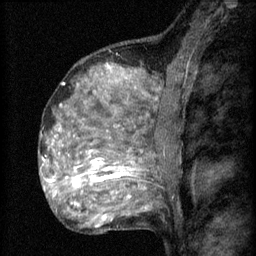
Breast MRI (dynamic contrast-enhanced), one sagittal slice; position 40 of 60 along the scan axis; 3 images stored at this slice position (order not interpretable as contrast timing); 1.5 T; TE 4.2 ms, TR 8.2 ms; 2 mm slice thickness; 256 × 256 image matrix, field of view 180 × 180 mm. Patient: female, 48 years.
Annotated regions visible in this slice (semi-automatically segmented with operator editing):
- analysis volume of interest (the breast-tissue region the enhancement analysis was run in; not a lesion): bounding box [x1, y1, x2, y2] px = [61, 138, 153, 201]
- tumour enhancement mask (voxels above the 70 % enhancement threshold inside the analysis volume of interest): [72, 150, 135, 199]